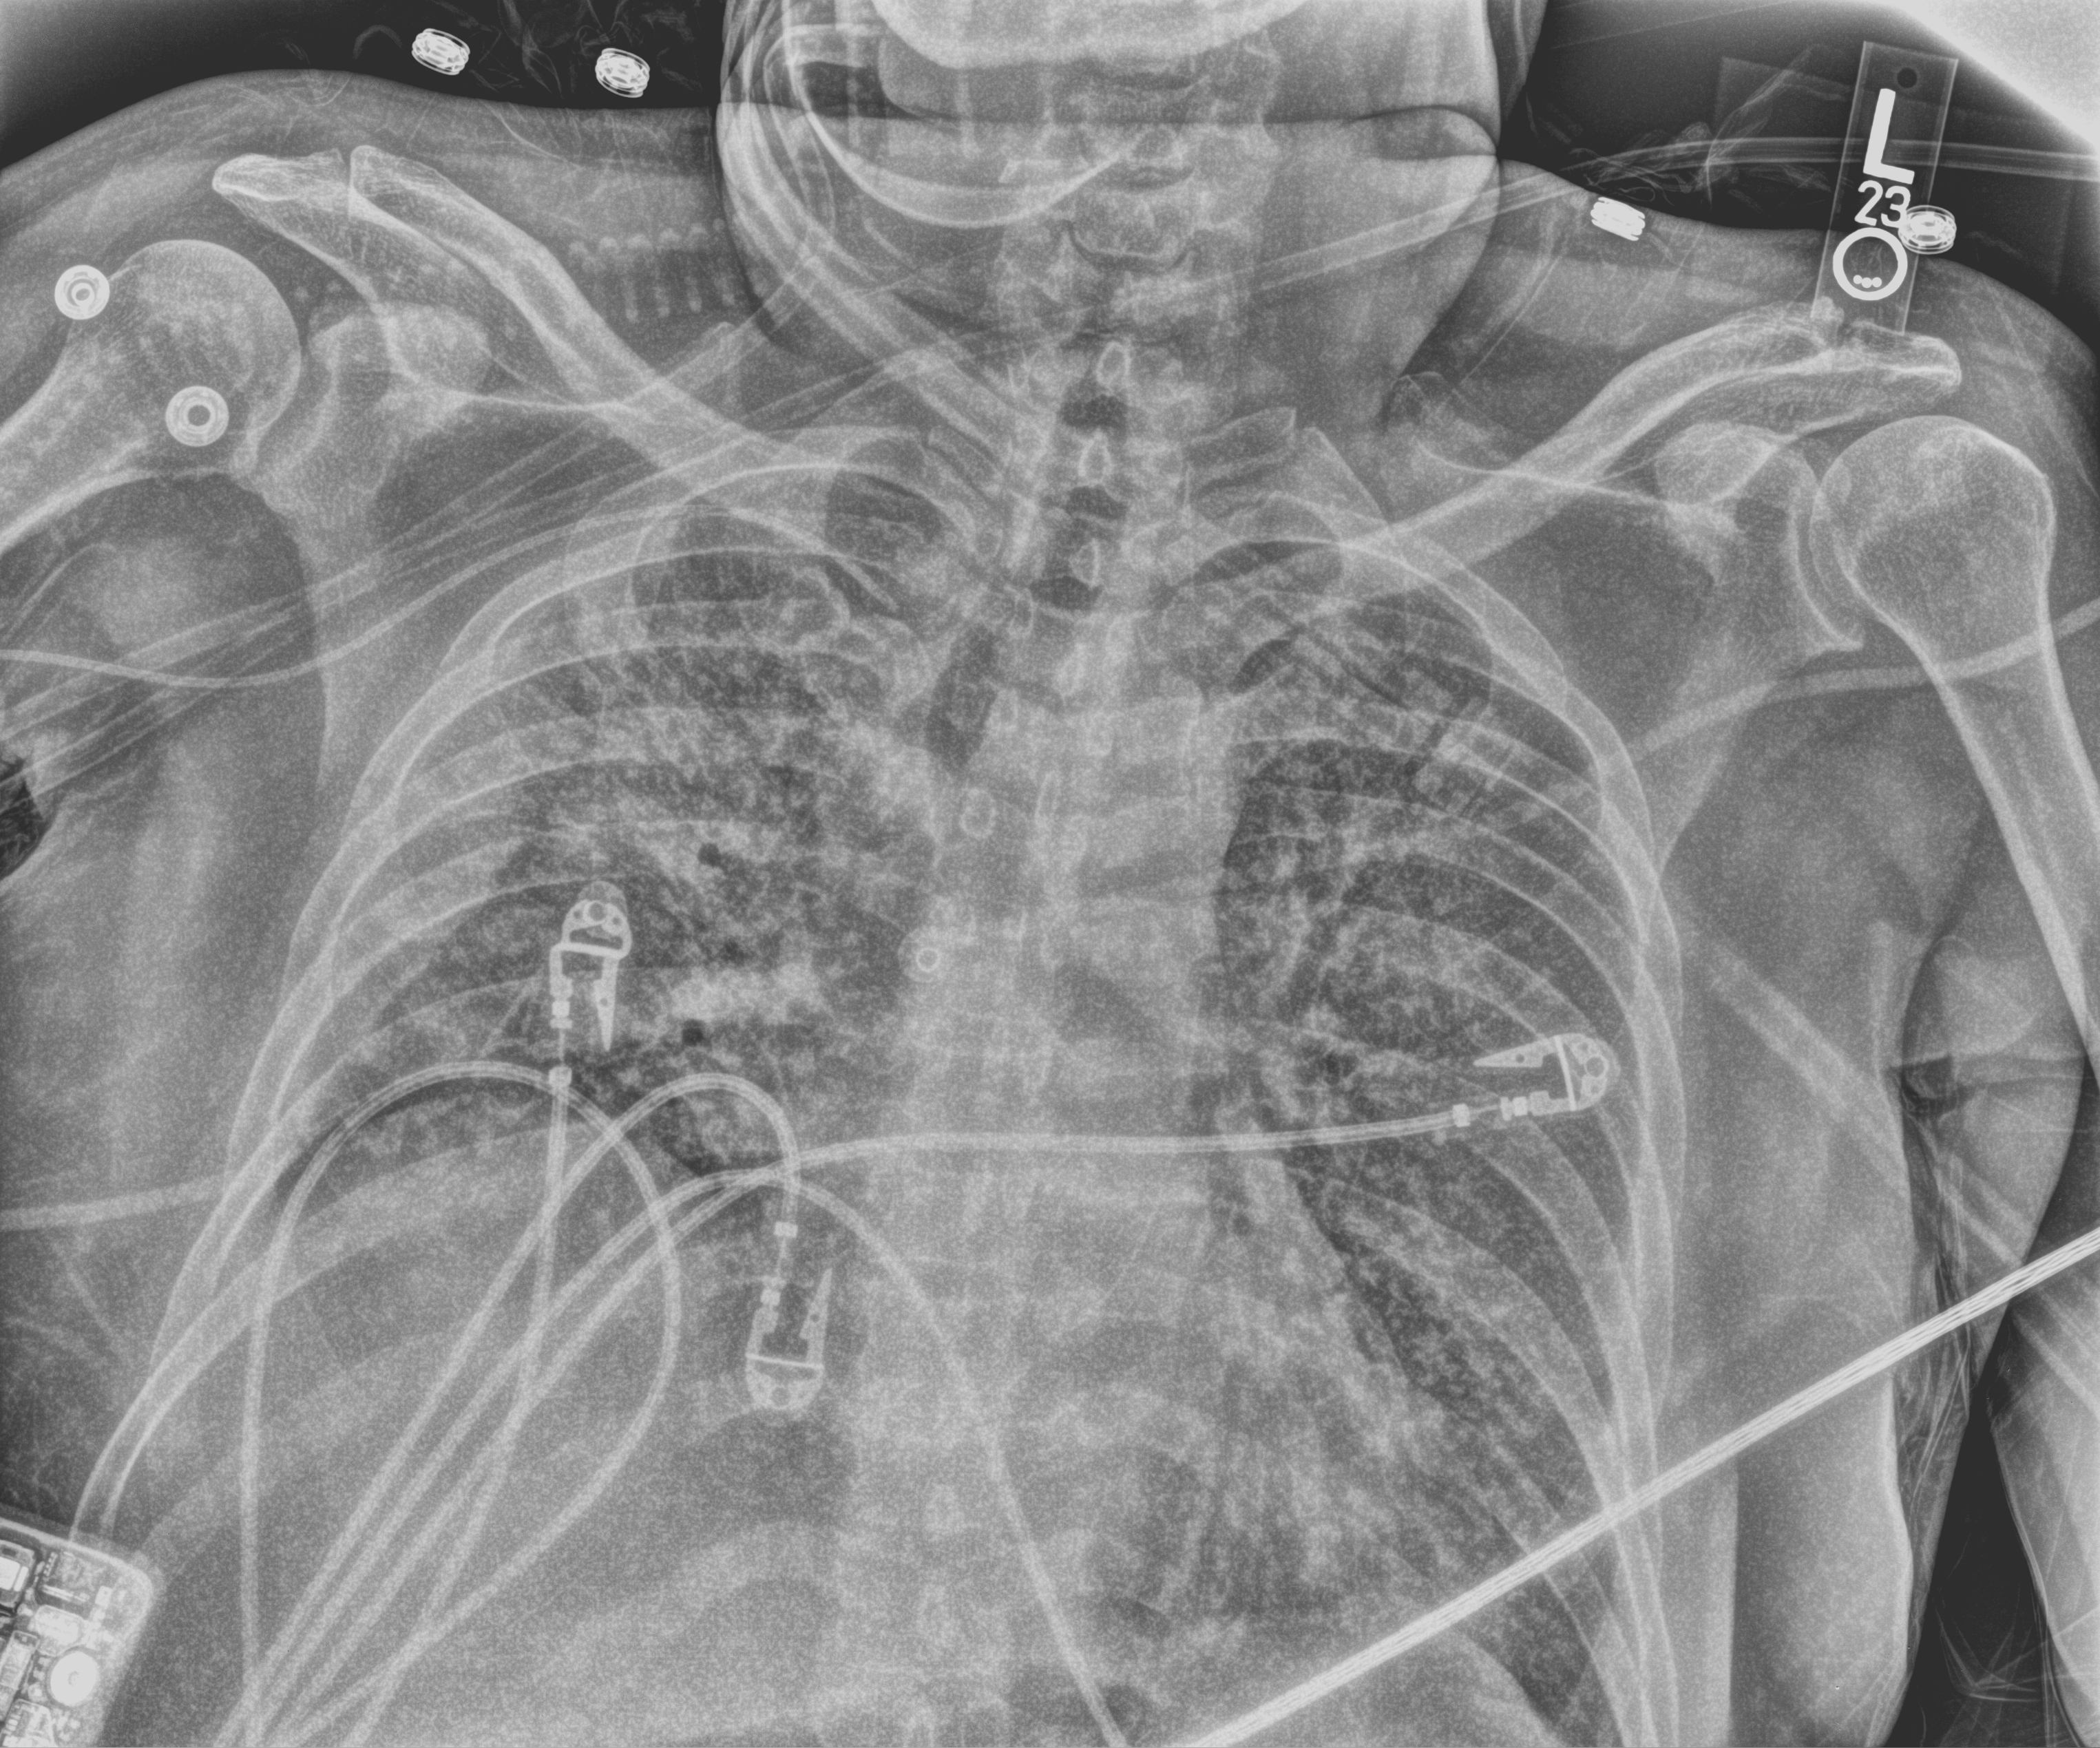
Bedside chest radiograph (computed radiography), anteroposterior (AP) projection. Patient hospitalised with COVID-19; male, aged 18–59 years.
Admission-level facts for this patient (not findings on this image; timing relative to this image not recorded): mechanically ventilated during this hospital stay: yes.